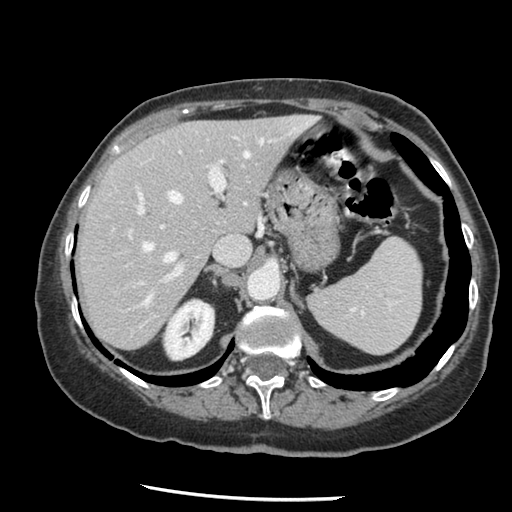
Contrast-enhanced abdominal CT, one axial slice; slice 94 of 148 in the series (ordered by position); reconstruction kernel STANDARD; 120 kVp; soft-tissue window (W 400 / L 40 HU); 2.5 mm slice thickness; 512 × 512 image matrix. Female patient, age 85 years. Case-level facts recorded for this patient, not image findings: diagnosis: colorectal cancer liver metastases, imaged before liver resection; multiple liver metastases: no; largest metastasis: 0.9 cm; disease in both lobes: no.
Structures marked on this image (manually delineated by an expert):
- hepatic veins: bounding box (x1, y1, x2, y2) in pixels: (143, 134, 291, 305)
- liver: (78, 116, 314, 349)
- planned liver remnant (the part of the liver to remain after resection): (78, 116, 314, 349)
- portal vein (with intrahepatic branches): (129, 140, 227, 285)